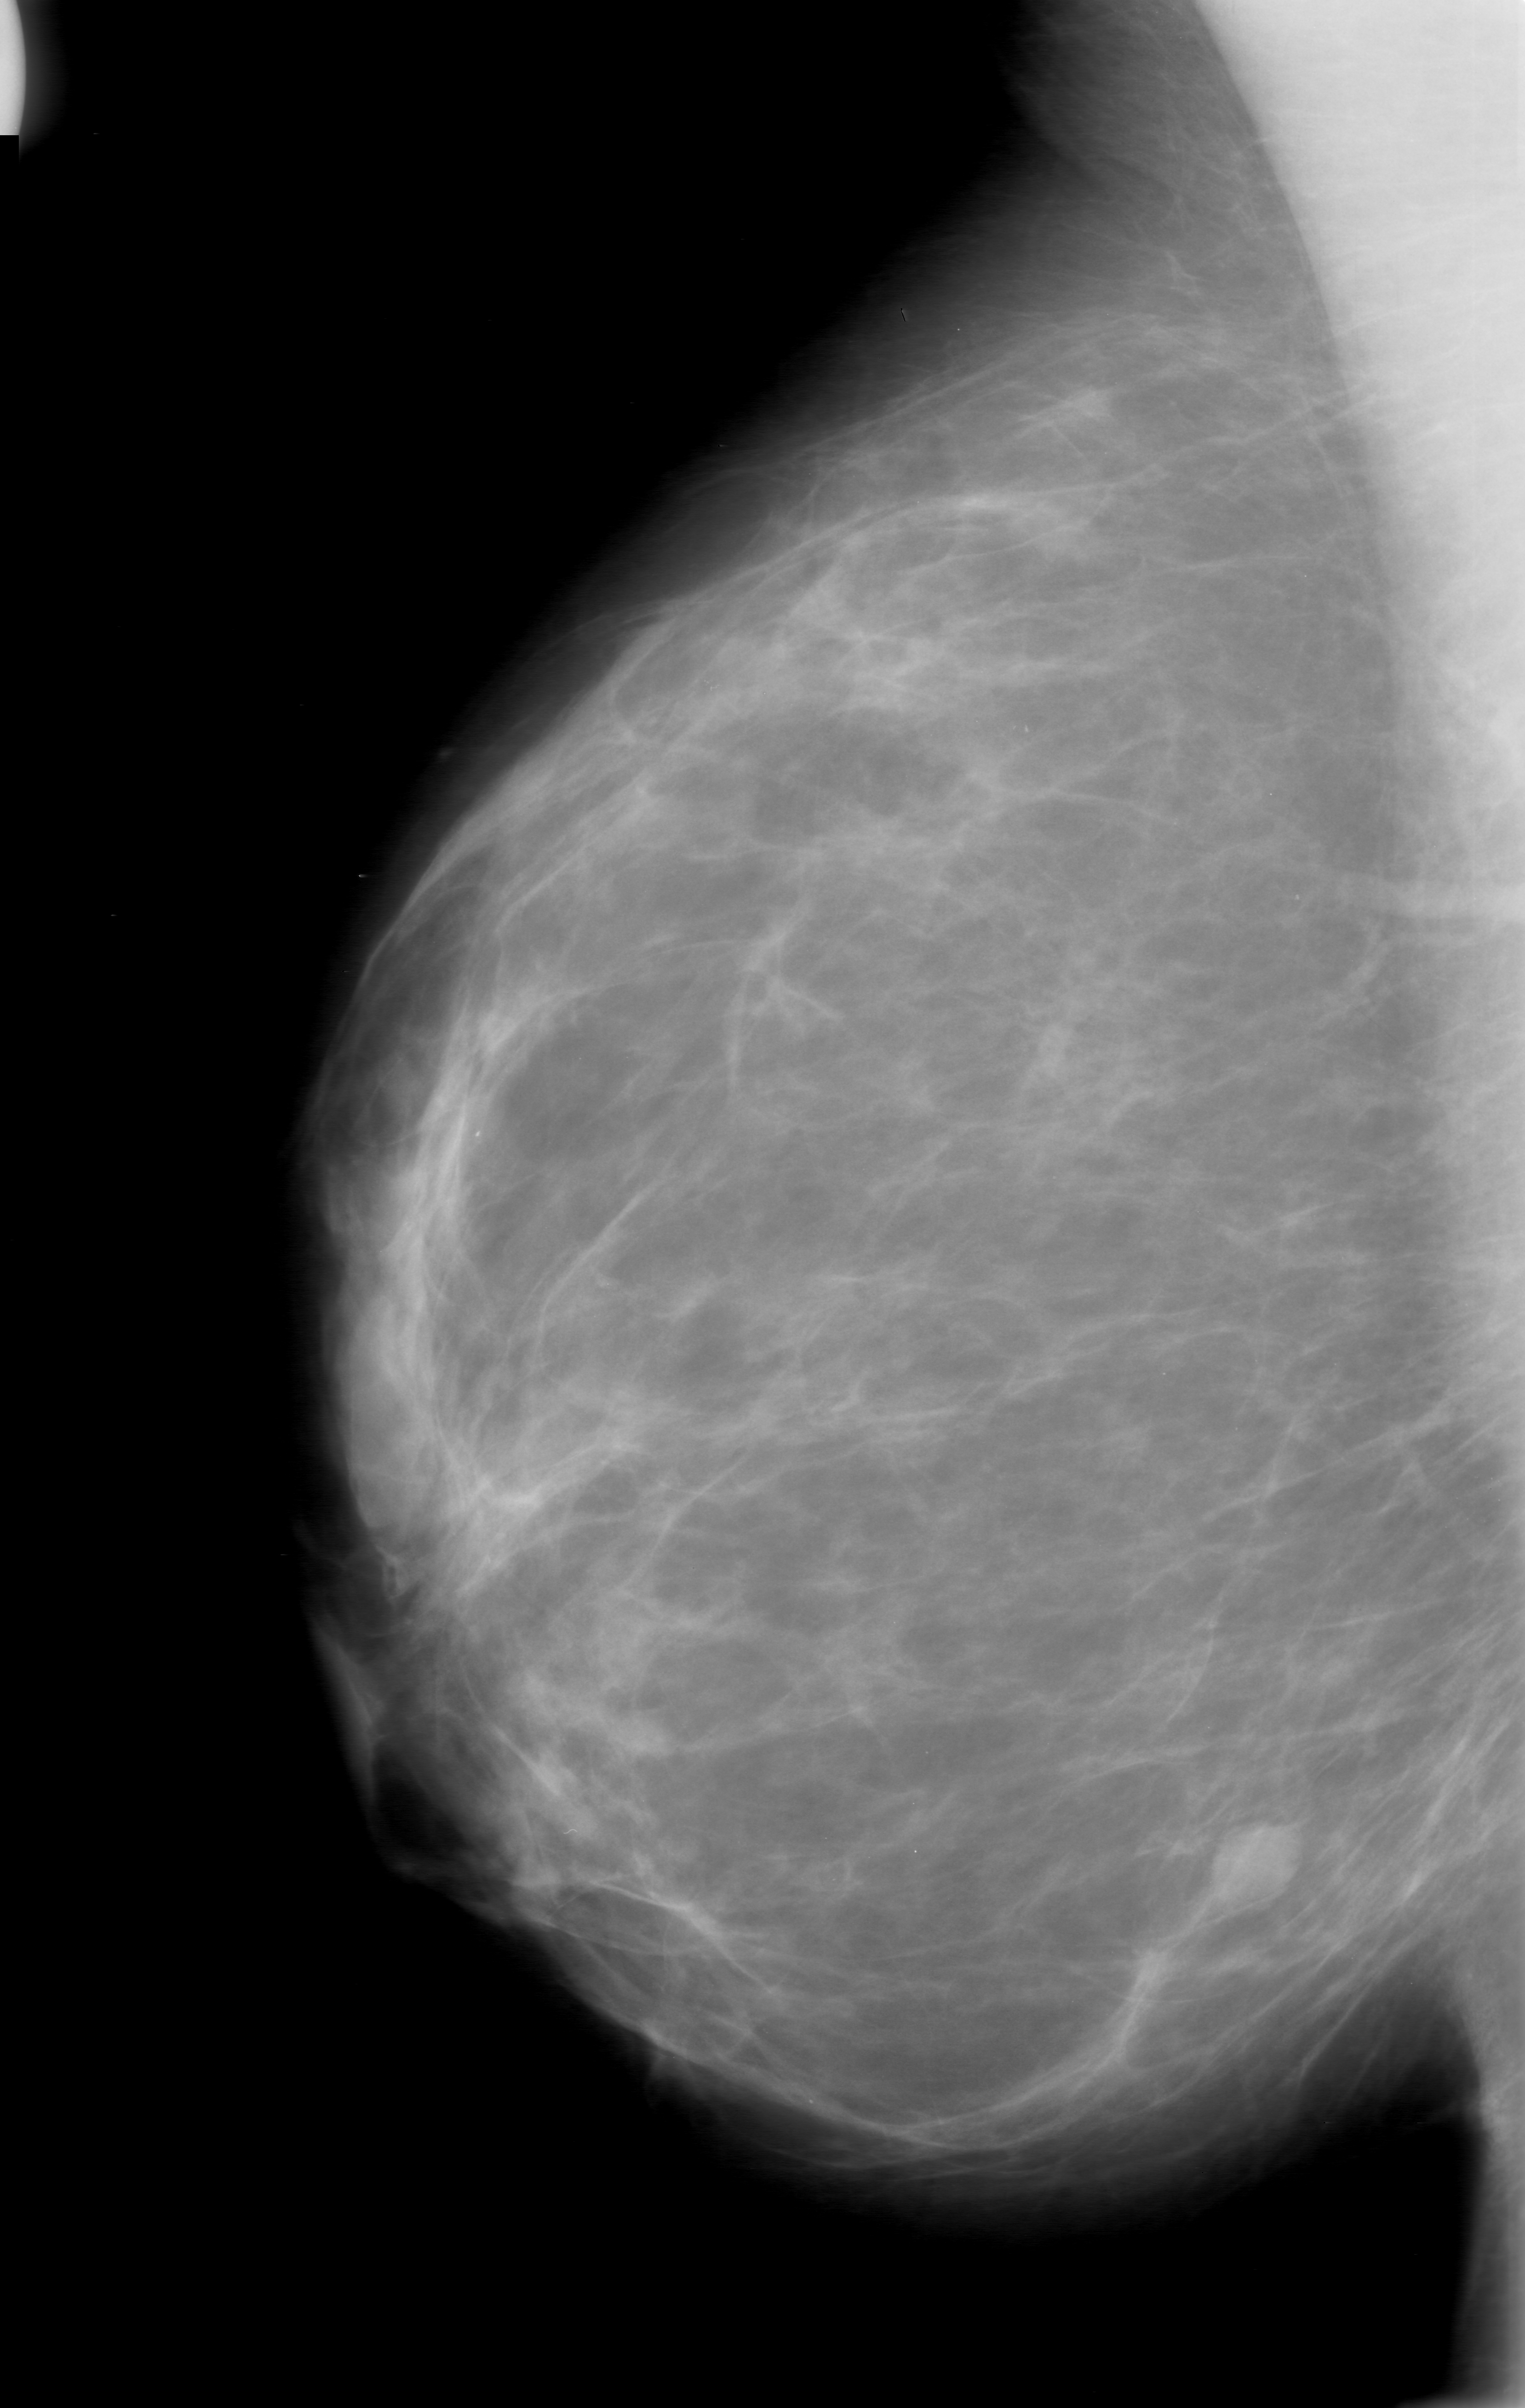
Mammogram (digitized film); right breast; mediolateral oblique (MLO) view; breast composition: scattered fibroglandular densities (BI-RADS density category 2 of 4).
- Mass, shape oval, margins ill defined; BI-RADS assessment category 0 (incomplete: needs additional imaging); pathology (as recorded): benign.